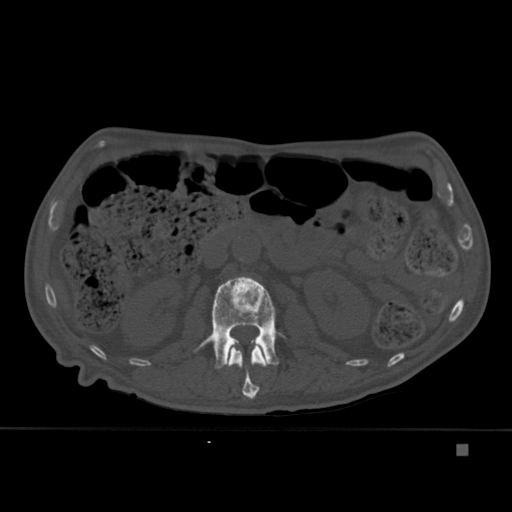
CT including the spine, one axial slice; slice 168 of 451 in the series (ordered by position); bone window (W 1800 / L 400 HU); 1.5 mm slice thickness; 512 × 512 image matrix. Patient: male, 75 years. From the clinical record (not read from this slice): primary cancer: prostate.
Structures marked on this image (semi-automatic segmentation, software-assisted and operator-edited):
- L1 vertebra: bounding box <227,345,268,400> (left, top, right, bottom; pixels)
- L2 vertebra: <194,276,285,369>